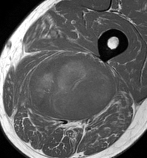
MRI of an extremity soft-tissue mass, one axial slice; slice 66 of 86 in the series (ordered by position); MR volume resampled by the dataset authors to the PET/CT grid (not the native acquisition matrix); 3.27 mm slice thickness; 147 × 158 image matrix, field of view 144 × 154 mm. Male patient. Case-level facts recorded for this patient, not image findings: histological type: undifferentiated pleomorphic liposarcoma; grade: high; site of the primary tumour: left thigh.
Outlined on this slice (expert contour drawn on MRI and transferred to this co-registered scan by the dataset authors):
- gross tumour volume including surrounding oedema: bounding box [x1, y1, x2, y2] px = [18, 56, 115, 128]
- gross tumour volume (mass): [28, 56, 115, 120]